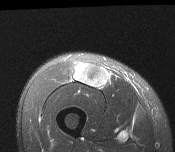
MRI of an extremity soft-tissue mass, one axial slice. Position 51 of 116 along the scan axis. T2-weighted fat-saturated. MR volume resampled by the dataset authors to the PET/CT grid (not the native acquisition matrix). 175 × 152 image matrix, field of view 171 × 148 mm. Male patient. Case-level facts recorded for this patient, not image findings: histological type: pleiomorphic leiomyosarcoma; grade: intermediate; site of the primary tumour: right thigh.
Annotated regions visible in this slice (expert contour drawn on MRI and transferred to this co-registered scan by the dataset authors):
- gross tumour volume including surrounding oedema: box from (x=74, y=63) to (x=107, y=87) px